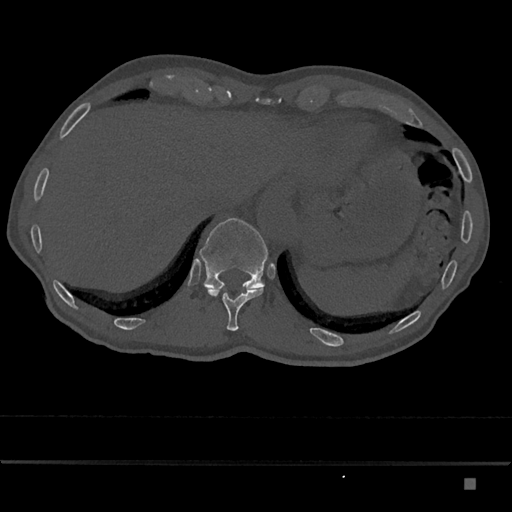
CT including the spine, one axial slice; slice 647 of 797 in the series (ordered by position); reconstruction kernel Br40s/3; bone window (W 1800 / L 400 HU); 512 × 512 image matrix, field of view 390 × 390 mm. Male patient, age 72 years. From the clinical record (not read from this slice): primary cancer: prostate.
Structures marked on this image (semi-automatic segmentation, software-assisted and operator-edited):
- T11 vertebra: box from (x=208, y=286) to (x=265, y=331) px
- T12 vertebra: (x=199, y=218)–(x=268, y=289)